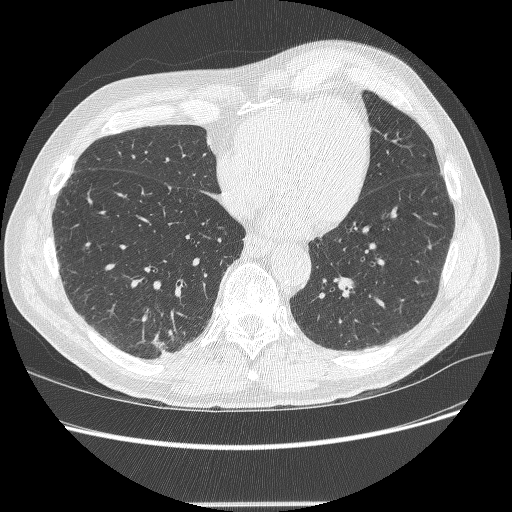
Low-dose screening chest CT, axial slice, second annual screen, lung window (W 1500 / L -600 HU), 1.25 mm slice thickness, lung (sharp) reconstruction kernel (BONE), slice 78 of 245 in the series. Male, age 71 years at enrolment.
Expert-annotated lung lesion, bounding box (x1, y1, x2, y2) in pixels: (137, 322, 191, 366). The screening reader recorded 5 non-calcified nodules or masses ≥4 mm on this exam (right lower lobe, right lower lobe, right upper lobe, right upper lobe, right upper lobe); which of them this box marks is not recorded. Official screen result: positive, change unspecified: nodule(s) >= 4 mm or enlarging nodule(s), mass(es), or other non-specific abnormalities suspicious for lung cancer. Later outcome: lung cancer diagnosed 7 days after this screen — squamous cell carcinoma, NOS, right lower lobe, moderately differentiated (G2), stage IA (AJCC 6th edition), 27 mm at pathology.